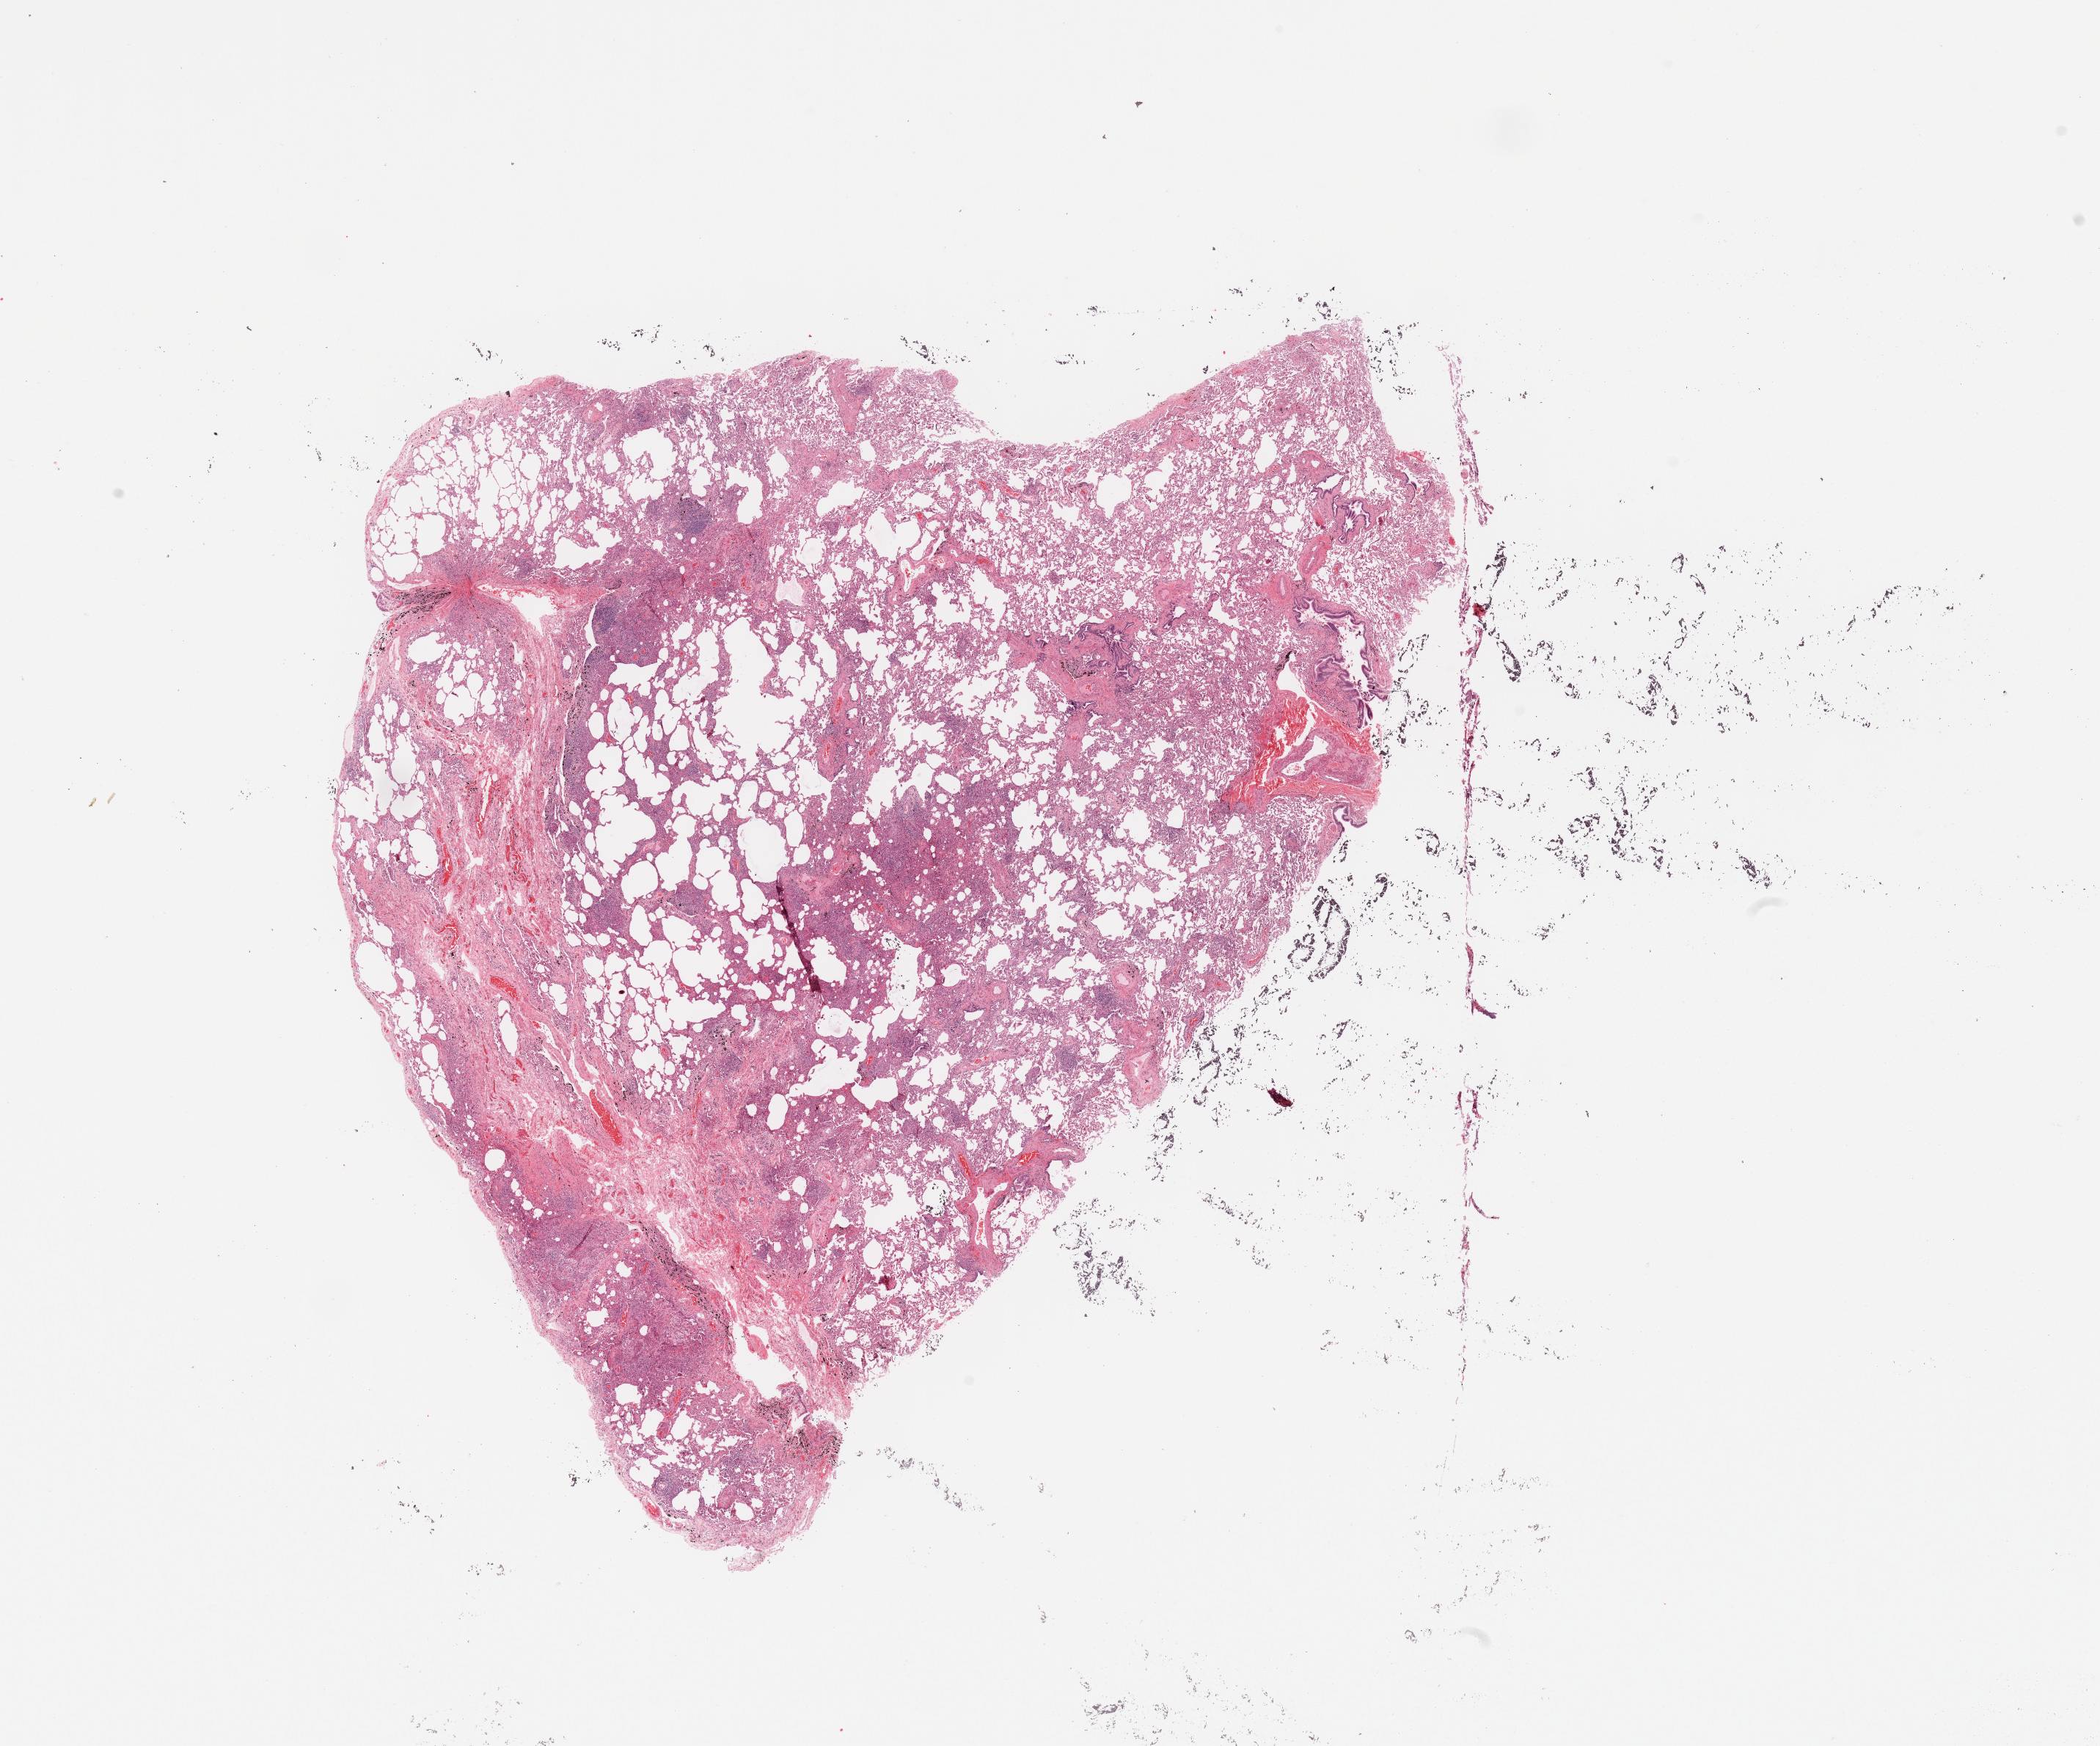
Whole-slide histology image, Hematoxylin and eosin (H&E) stained — whole scanned area (about 22.6 x 18.8 mm) shown as a low-resolution overview; normal (non-tumour) tissue sample, sampled site: lung. Patient: male, age 68 years.
This section: normal (non-tumour) tissue from the same patient. Patient diagnosis: Adenocarcinoma, NOS.